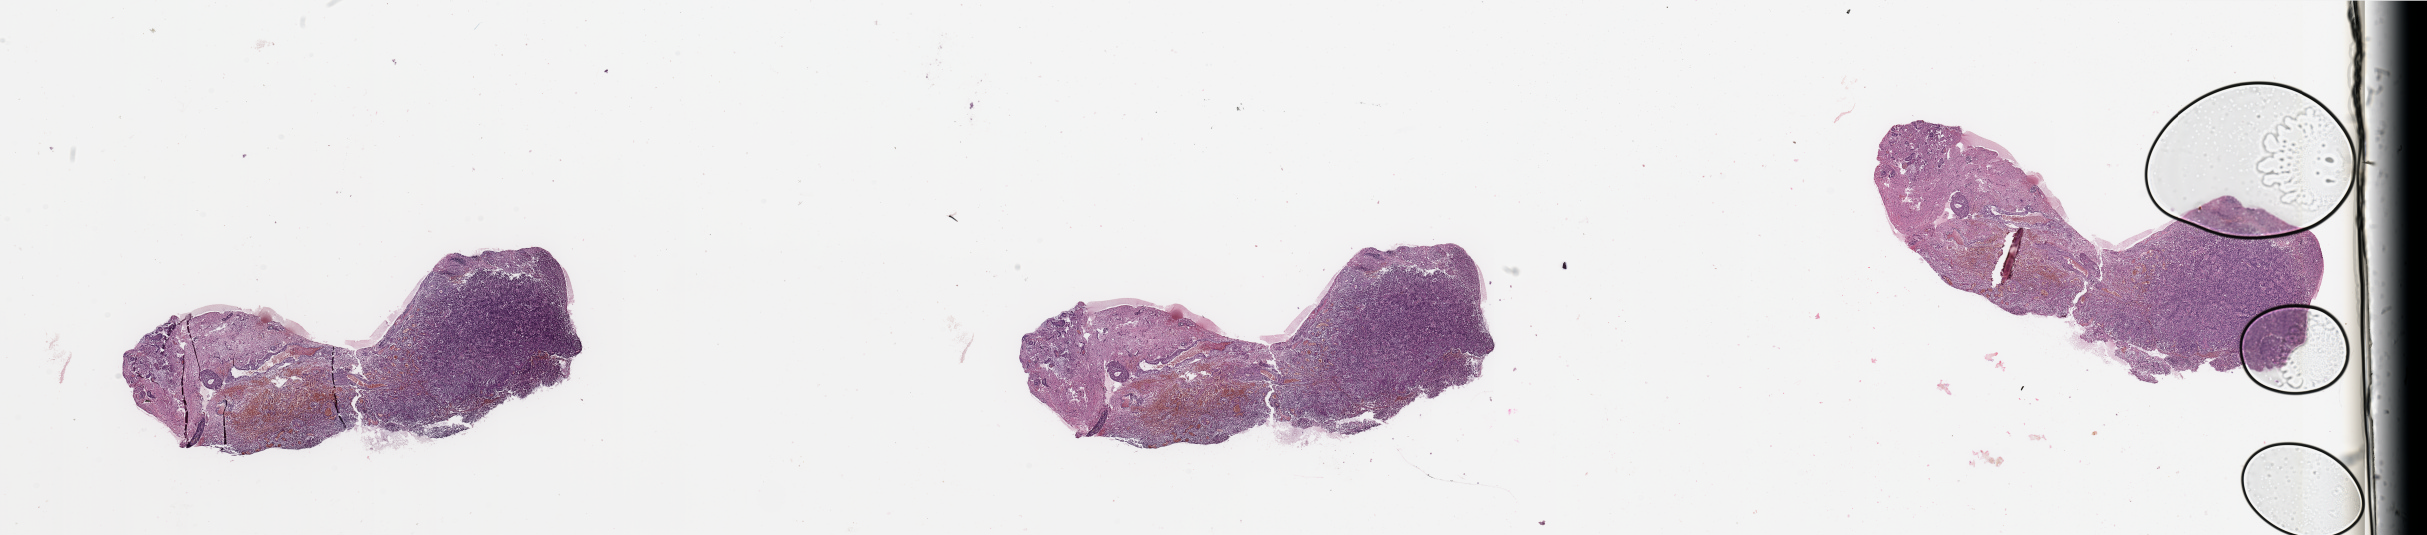
Whole-slide histology image, Hematoxylin and eosin (H&E) stained — a low-resolution overview of the entire scanned area, about 38.4 x 8.5 mm (acquisition: 20x scan); tumour tissue sample, sampled site: brain. 58-year-old female patient. Slide review estimates, as recorded: tumour nuclei 70%, necrosis 5%.
Diagnosis: Glioblastoma.